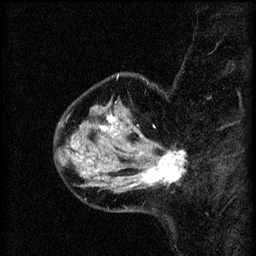
Breast MRI (dynamic contrast-enhanced), one sagittal slice. Position 15 of 60 along the scan axis. 3 images stored at this slice position (order not interpretable as contrast timing). 1.5 T. TE 4.2 ms, TR 8.2 ms. 2 mm slice thickness. 256 × 256 image matrix, field of view 180 × 180 mm. Female patient, age 37 years.
Structures marked on this image (semi-automatic segmentation, software-assisted and operator-edited):
- analysis volume of interest (the breast-tissue region the enhancement analysis was run in; not a lesion): bounding box [x1, y1, x2, y2] px = [124, 138, 186, 191]
- tumour enhancement mask (voxels above the 70 % enhancement threshold inside the analysis volume of interest): [125, 150, 186, 189]